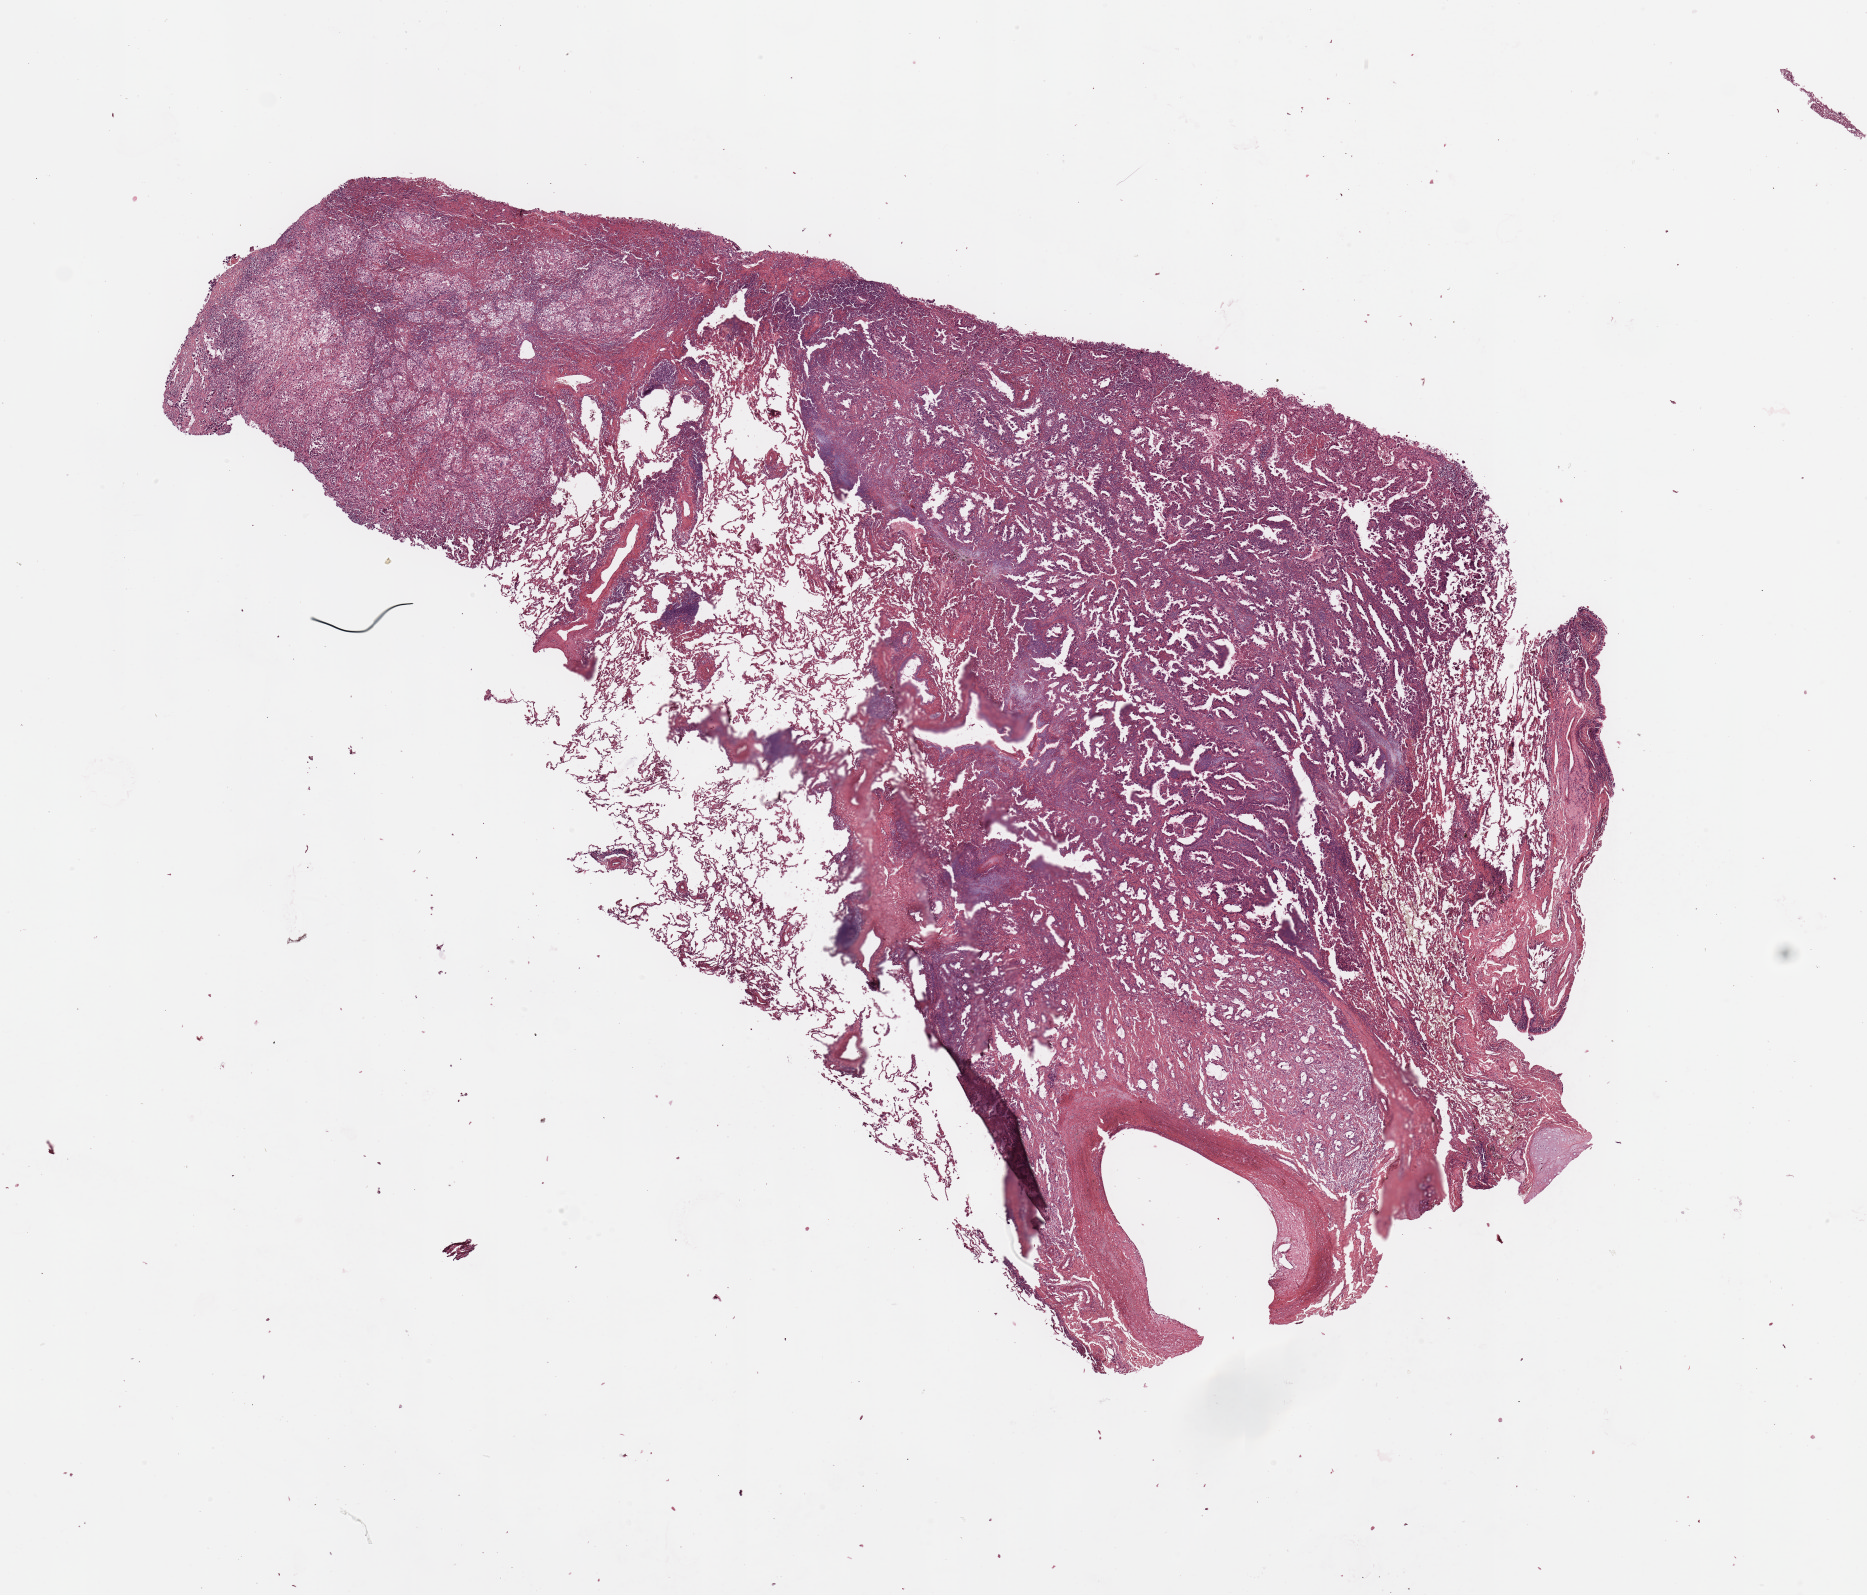
H&E-stained whole-slide image, whole scanned area (about 14.8 x 12.6 mm, from a 20x scan) shown as a low-resolution overview. Lung, tumour tissue. 63-year-old male patient. Histologic grade: G2 (moderately differentiated).
AJCC pathologic stage: IIIA. Primary tumour site (as recorded): left upper lobe. Diagnosis: Adenocarcinoma, NOS.